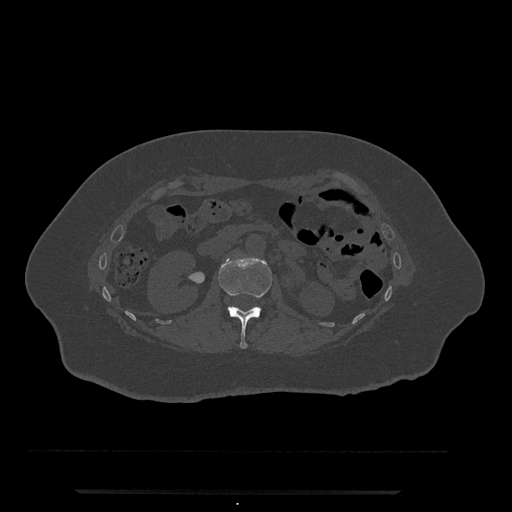
CT including the spine, one axial slice; position 93 of 797 along the scan axis; reconstruction kernel Br40s/3; bone window (W 1800 / L 400 HU); 512 × 512 image matrix, field of view 440 × 440 mm. Patient: female, 51 years. Case-level facts recorded for this patient, not image findings: primary cancer: neuro.
Structures marked on this image (semi-automatically segmented with operator editing):
- L1 vertebra: bounding box <218,255,272,349> (left, top, right, bottom; pixels)
- L2 vertebra: <229,306,234,307>